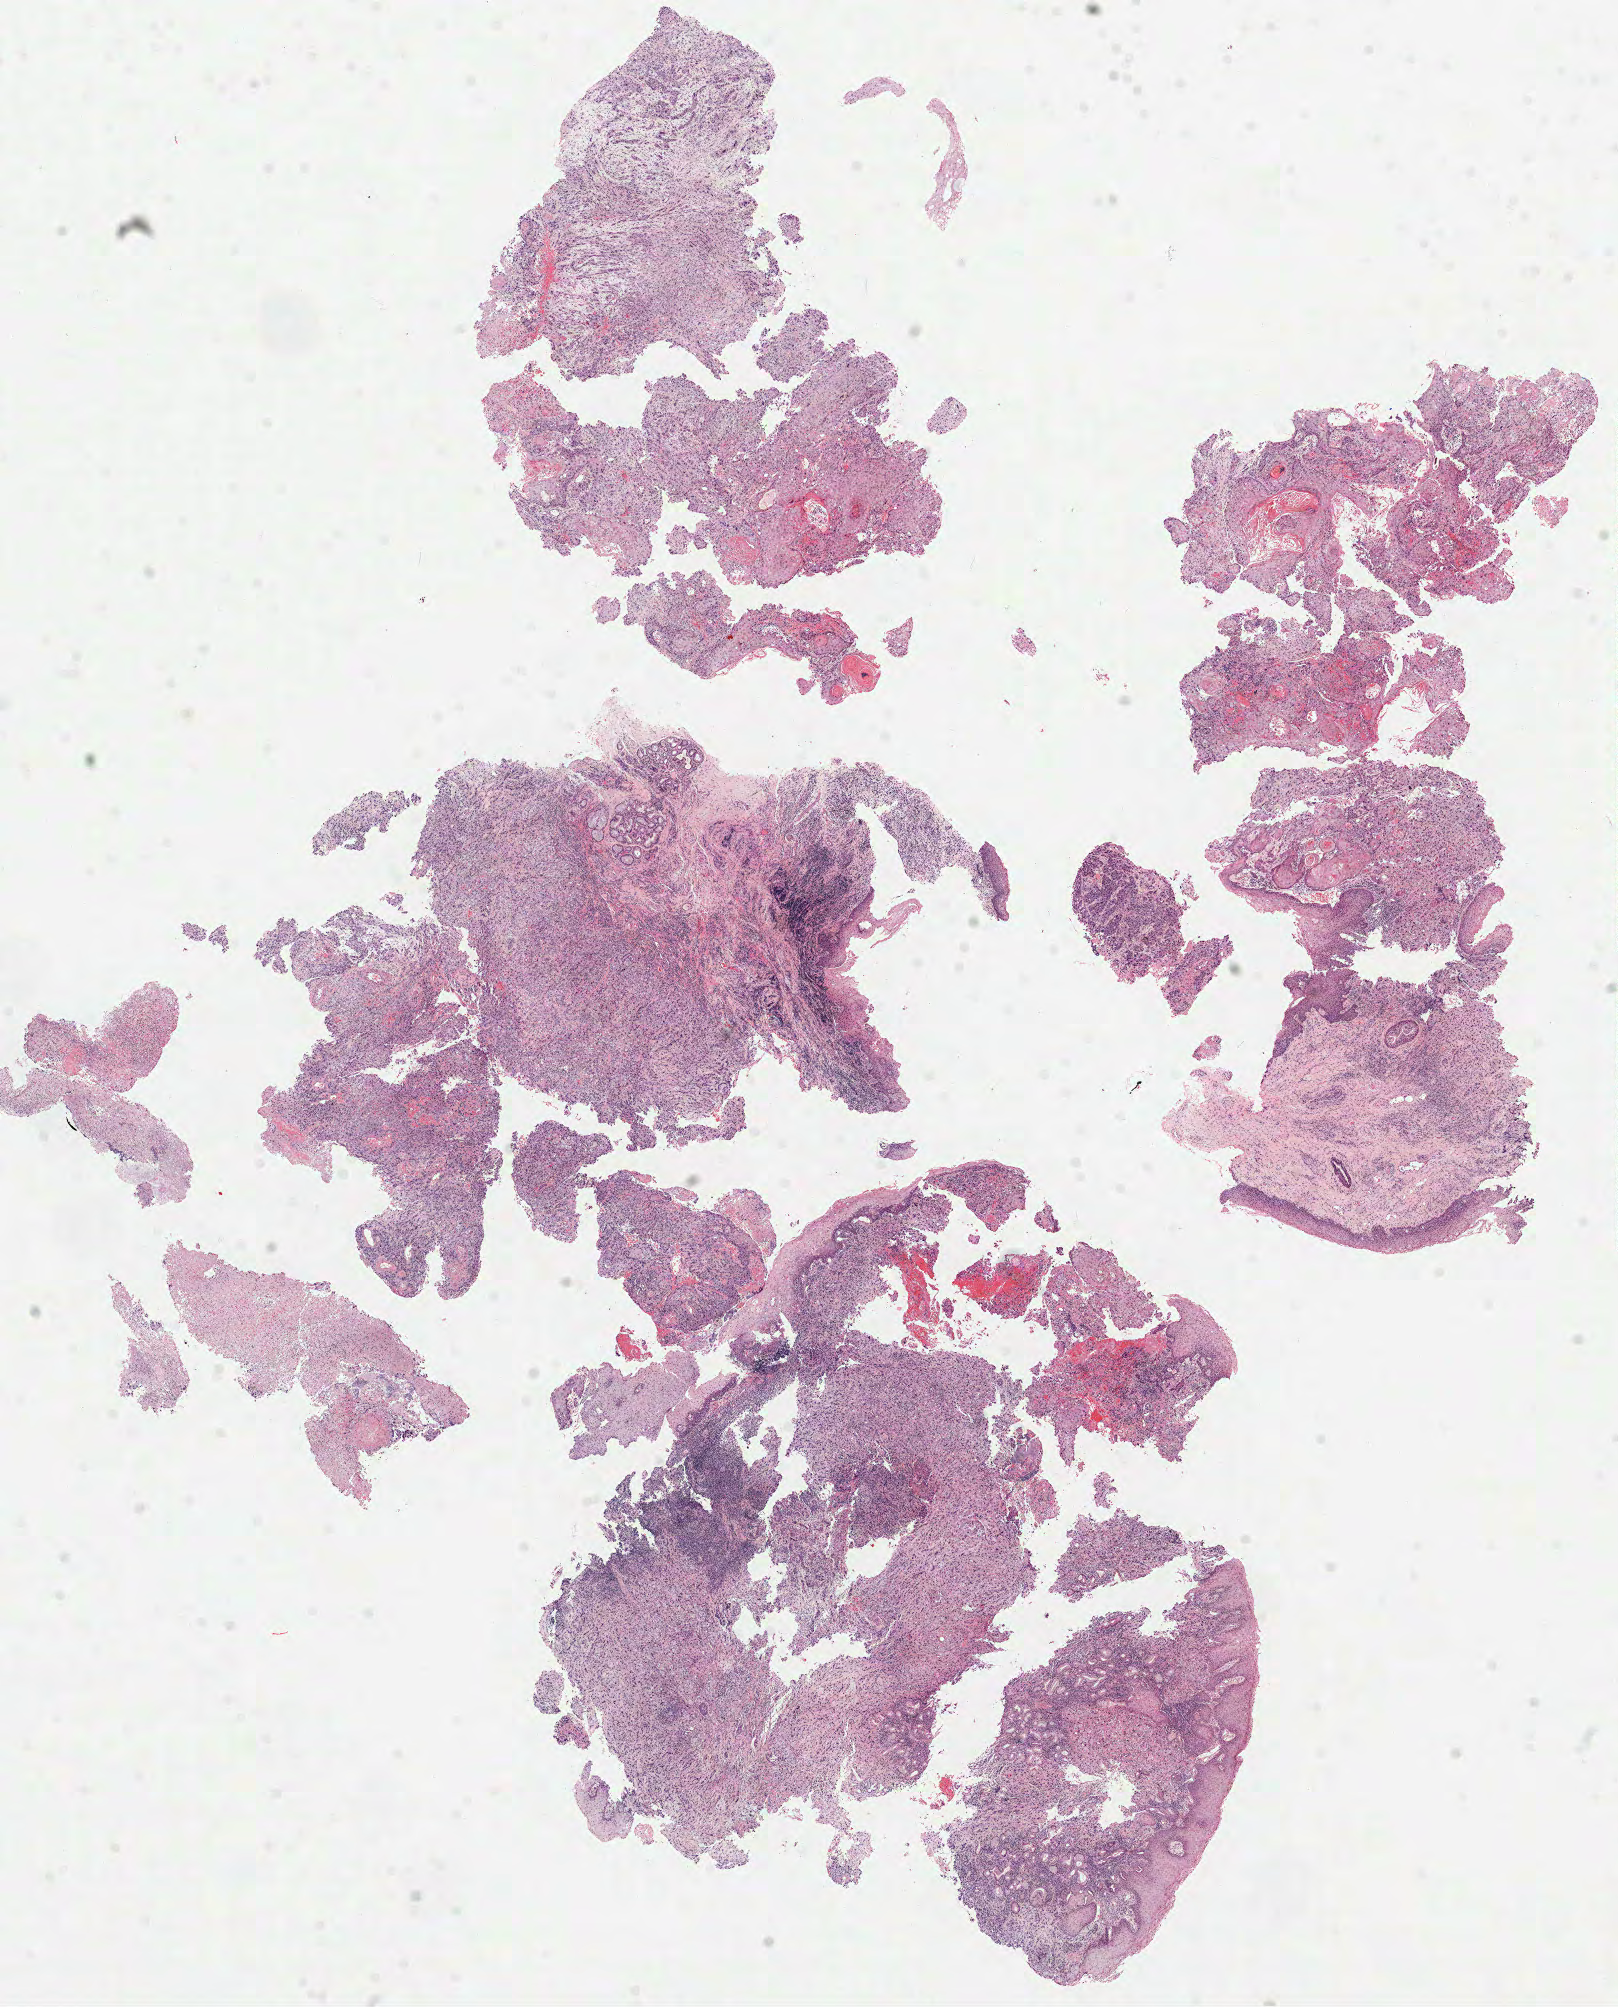
Digitized H&E-stained tissue section (whole slide), a low-resolution overview of the entire scanned area, about 13.1 x 16.2 mm (acquisition: 40x scan); FFPE section; primary tumour sample from the head and neck. Patient: male, age at initial diagnosis 53 years.
Diagnosis: Squamous cell carcinoma, NOS (larynx, NOS).